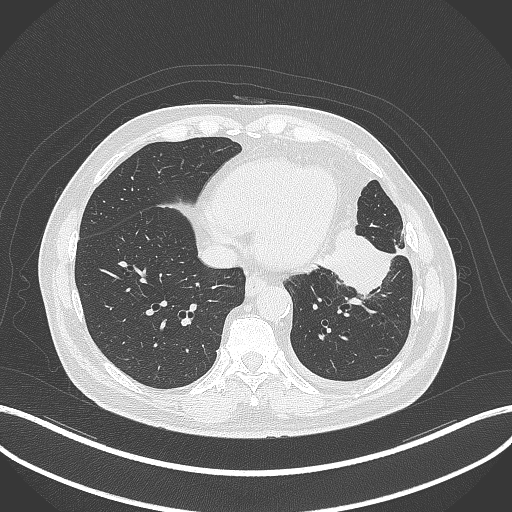
Chest CT, one axial slice; slice 109 of 230 in the series (ordered by position); reconstruction kernel B70f; lung window (W 1500 / L -600 HU); 1 mm slice thickness; 512 × 512 image matrix. Male patient, age 68 years. From the clinical record (not read from this slice): clinical TNM (as recorded): T2b N0 M0.
Outlined on this slice (bounding box drawn by a radiologist):
- lung tumour (recorded histology: squamous cell carcinoma): bounding box (x1, y1, x2, y2) in pixels: (321, 226, 397, 294)